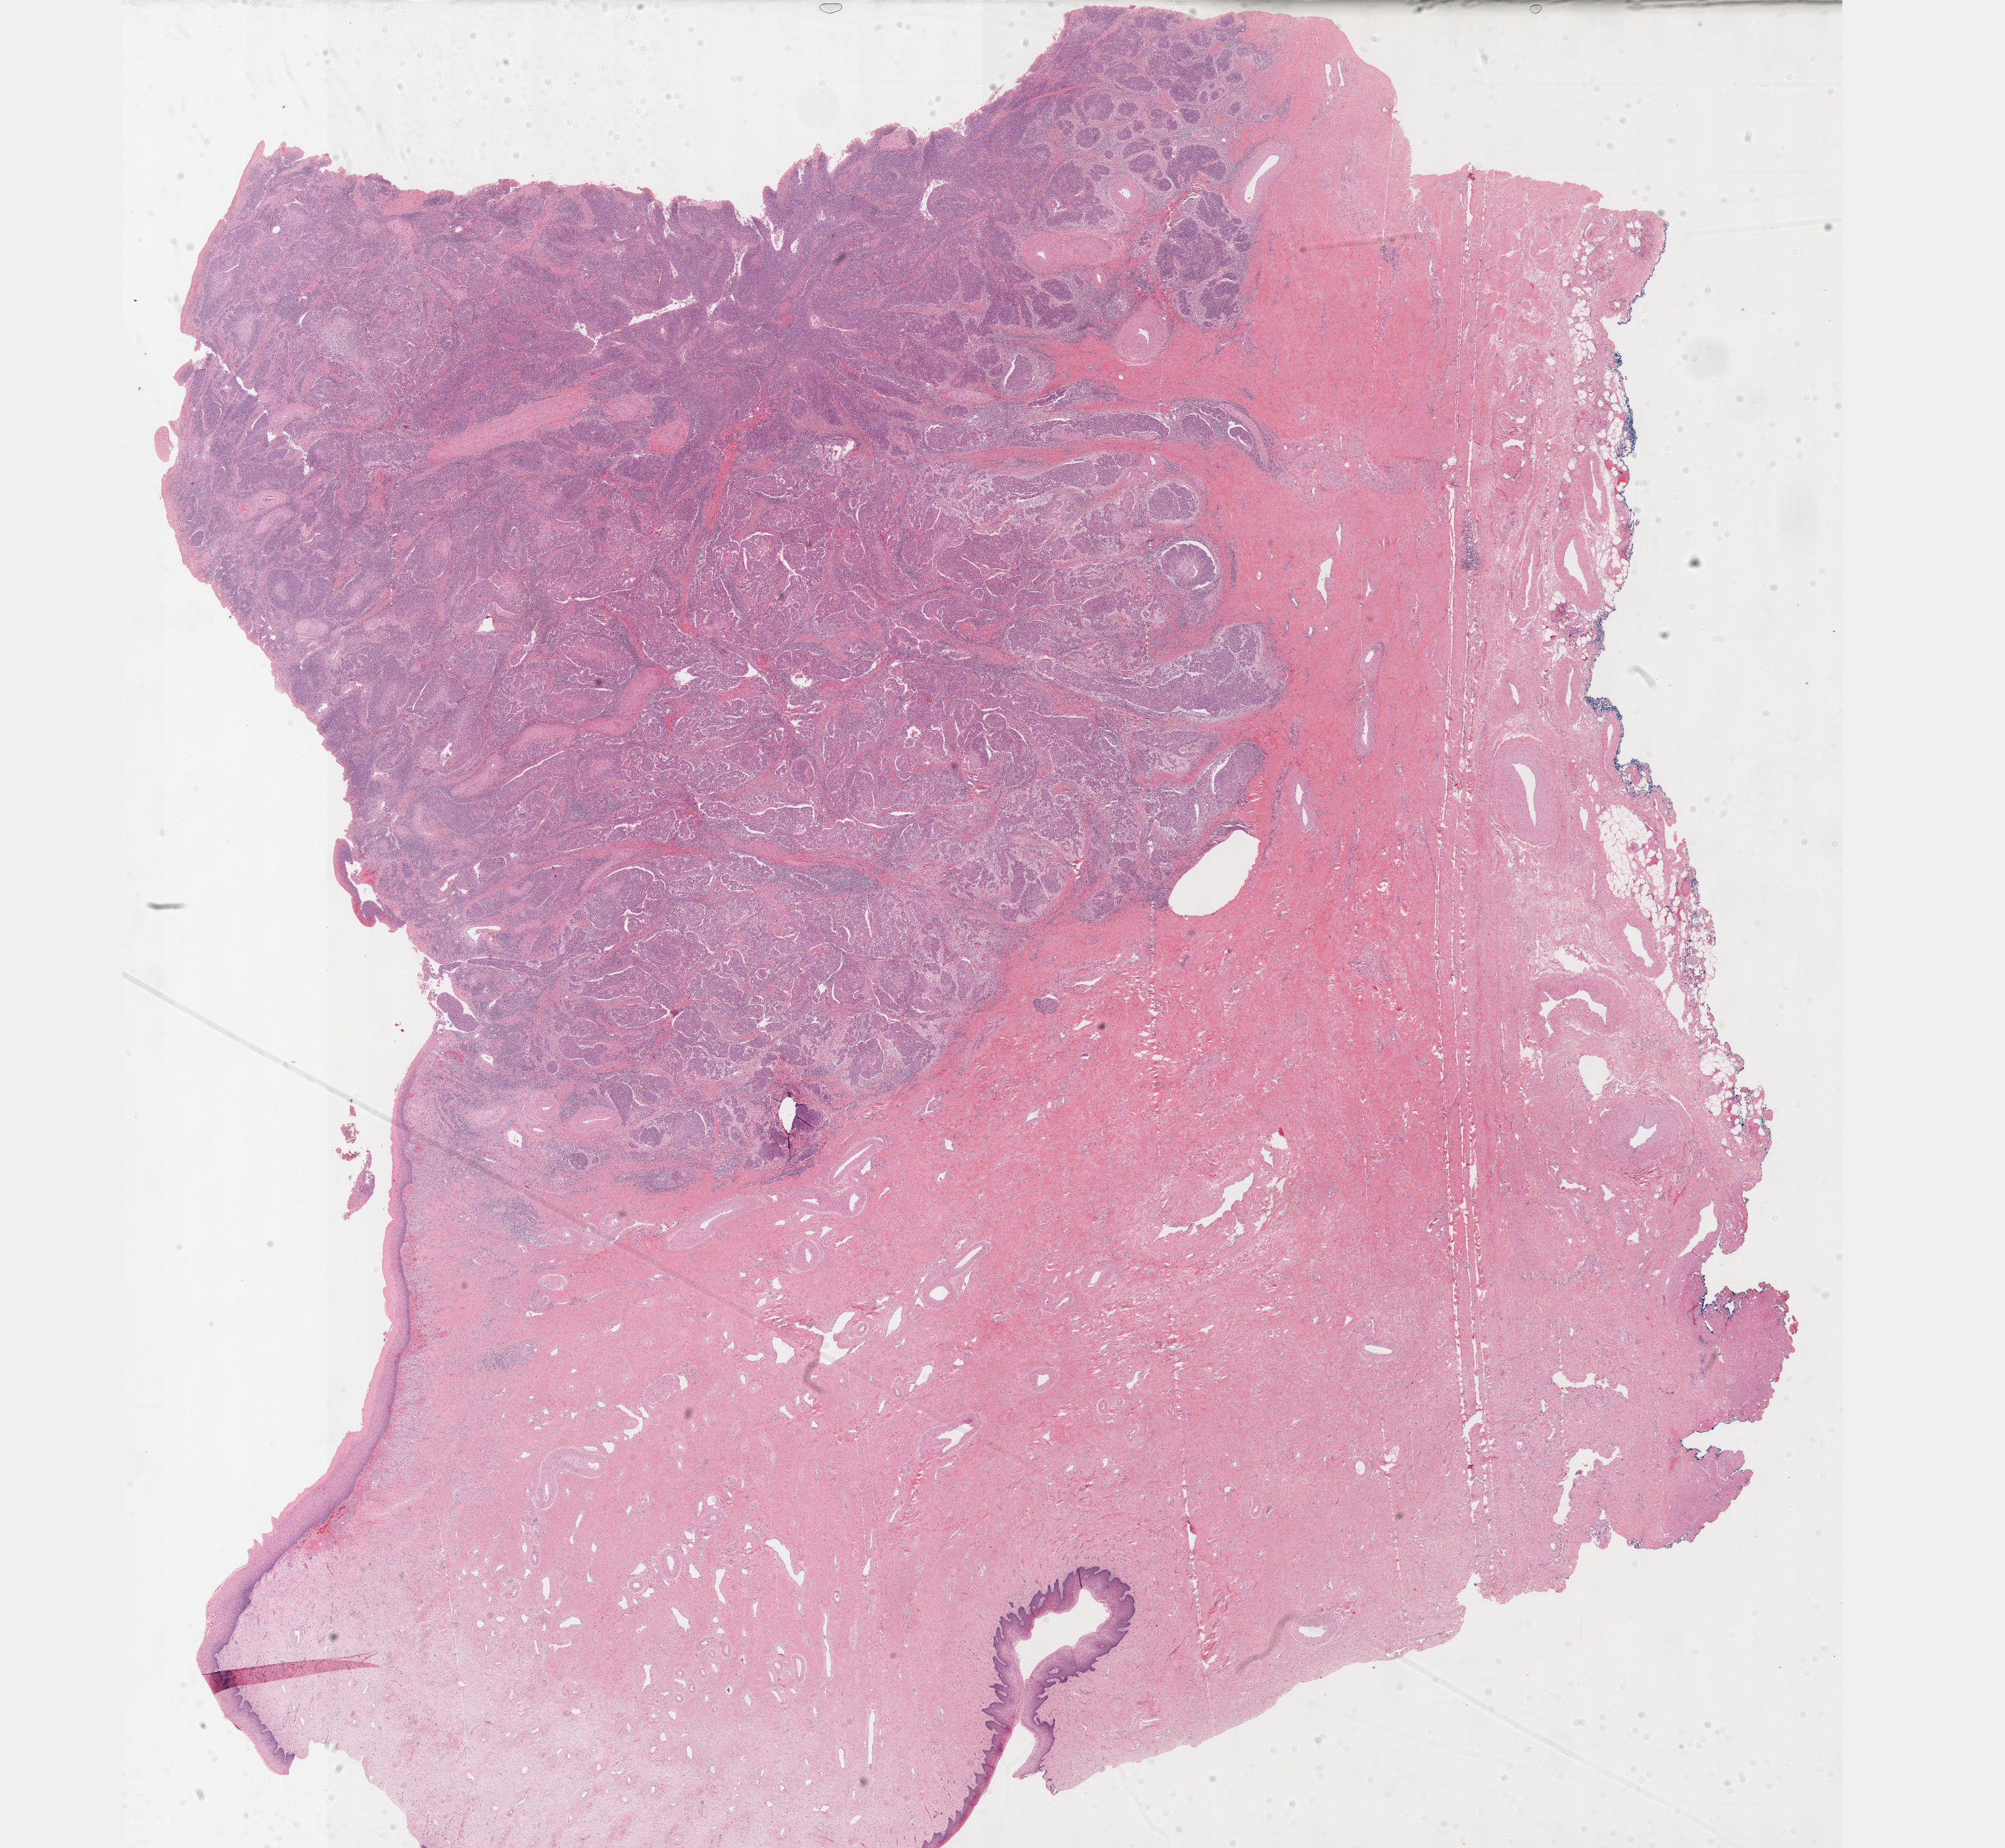
Digitized H&E-stained tissue section (whole slide) — shown as a low-resolution overview of the whole scanned area (about 24.6 x 22.7 mm, from a 40x scan). Formalin-fixed paraffin-embedded (FFPE) diagnostic section. Cervix, primary tumour sample. Female, age 44 years at initial diagnosis. Histologic grade: G2 (moderately differentiated).
FIGO stage: IB1. Histologic diagnosis: Squamous cell carcinoma, NOS (cervix uteri).